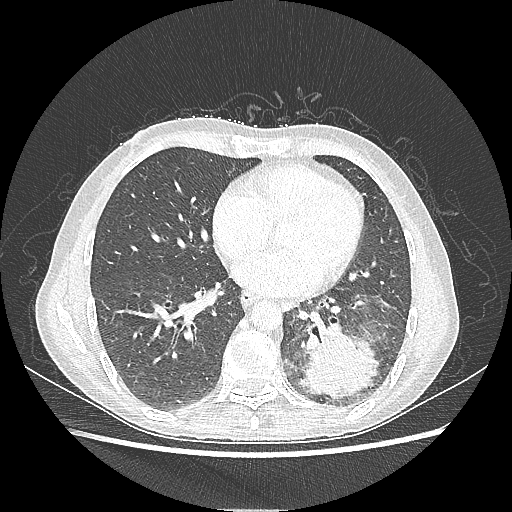
Chest CT, one axial slice. Slice 91 of 220 in the series (ordered by position). Reconstruction kernel LUNG. Lung window (W 1500 / L -600 HU). 1.25 mm slice thickness. 512 × 512 image matrix. Female patient, age 53 years. From the clinical record (not read from this slice): clinical TNM (as recorded): T3 N0 M0.
Structures marked on this image (bounding box drawn by a radiologist):
- lung tumour (recorded histology: adenocarcinoma): bounding box <298,325,380,401> (left, top, right, bottom; pixels)